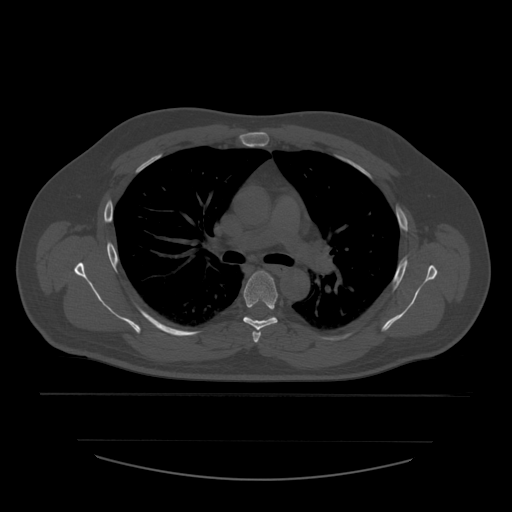
CT including the spine, one axial slice; slice 398 of 532 in the series (ordered by position); reconstruction kernel STANDARD; 120 kVp; bone window (W 1800 / L 400 HU); 1.25 mm slice thickness; 512 × 512 image matrix, field of view 441 × 441 mm. Patient age 44 years. From the clinical record (not read from this slice): primary cancer: soft tissue sarcoma.
Annotated regions visible in this slice (semi-automatically segmented with operator editing):
- T4 vertebra: bounding box [x1, y1, x2, y2] px = [253, 329, 261, 343]
- T5 vertebra: [244, 271, 278, 330]
- T6 vertebra: [269, 317, 273, 319]